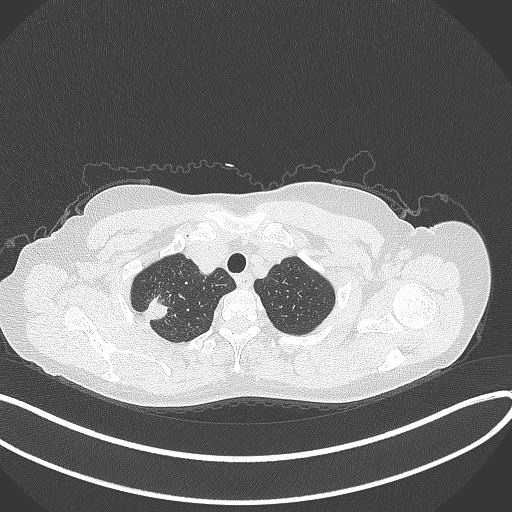
Chest CT, one axial slice; position 322 of 337 along the scan axis; reconstruction kernel B70f; 120 kVp; lung window (W 1500 / L -600 HU); 1 mm slice thickness; 512 × 512 image matrix. Patient: female, 50 years. From the clinical record (not read from this slice): clinical TNM (as recorded): T1c N0 M0; histopathological grade: G2-3.
Annotated regions visible in this slice (bounding box drawn by a radiologist):
- lung tumour (recorded histology: adenocarcinoma): bounding box [x1, y1, x2, y2] px = [140, 295, 170, 326]